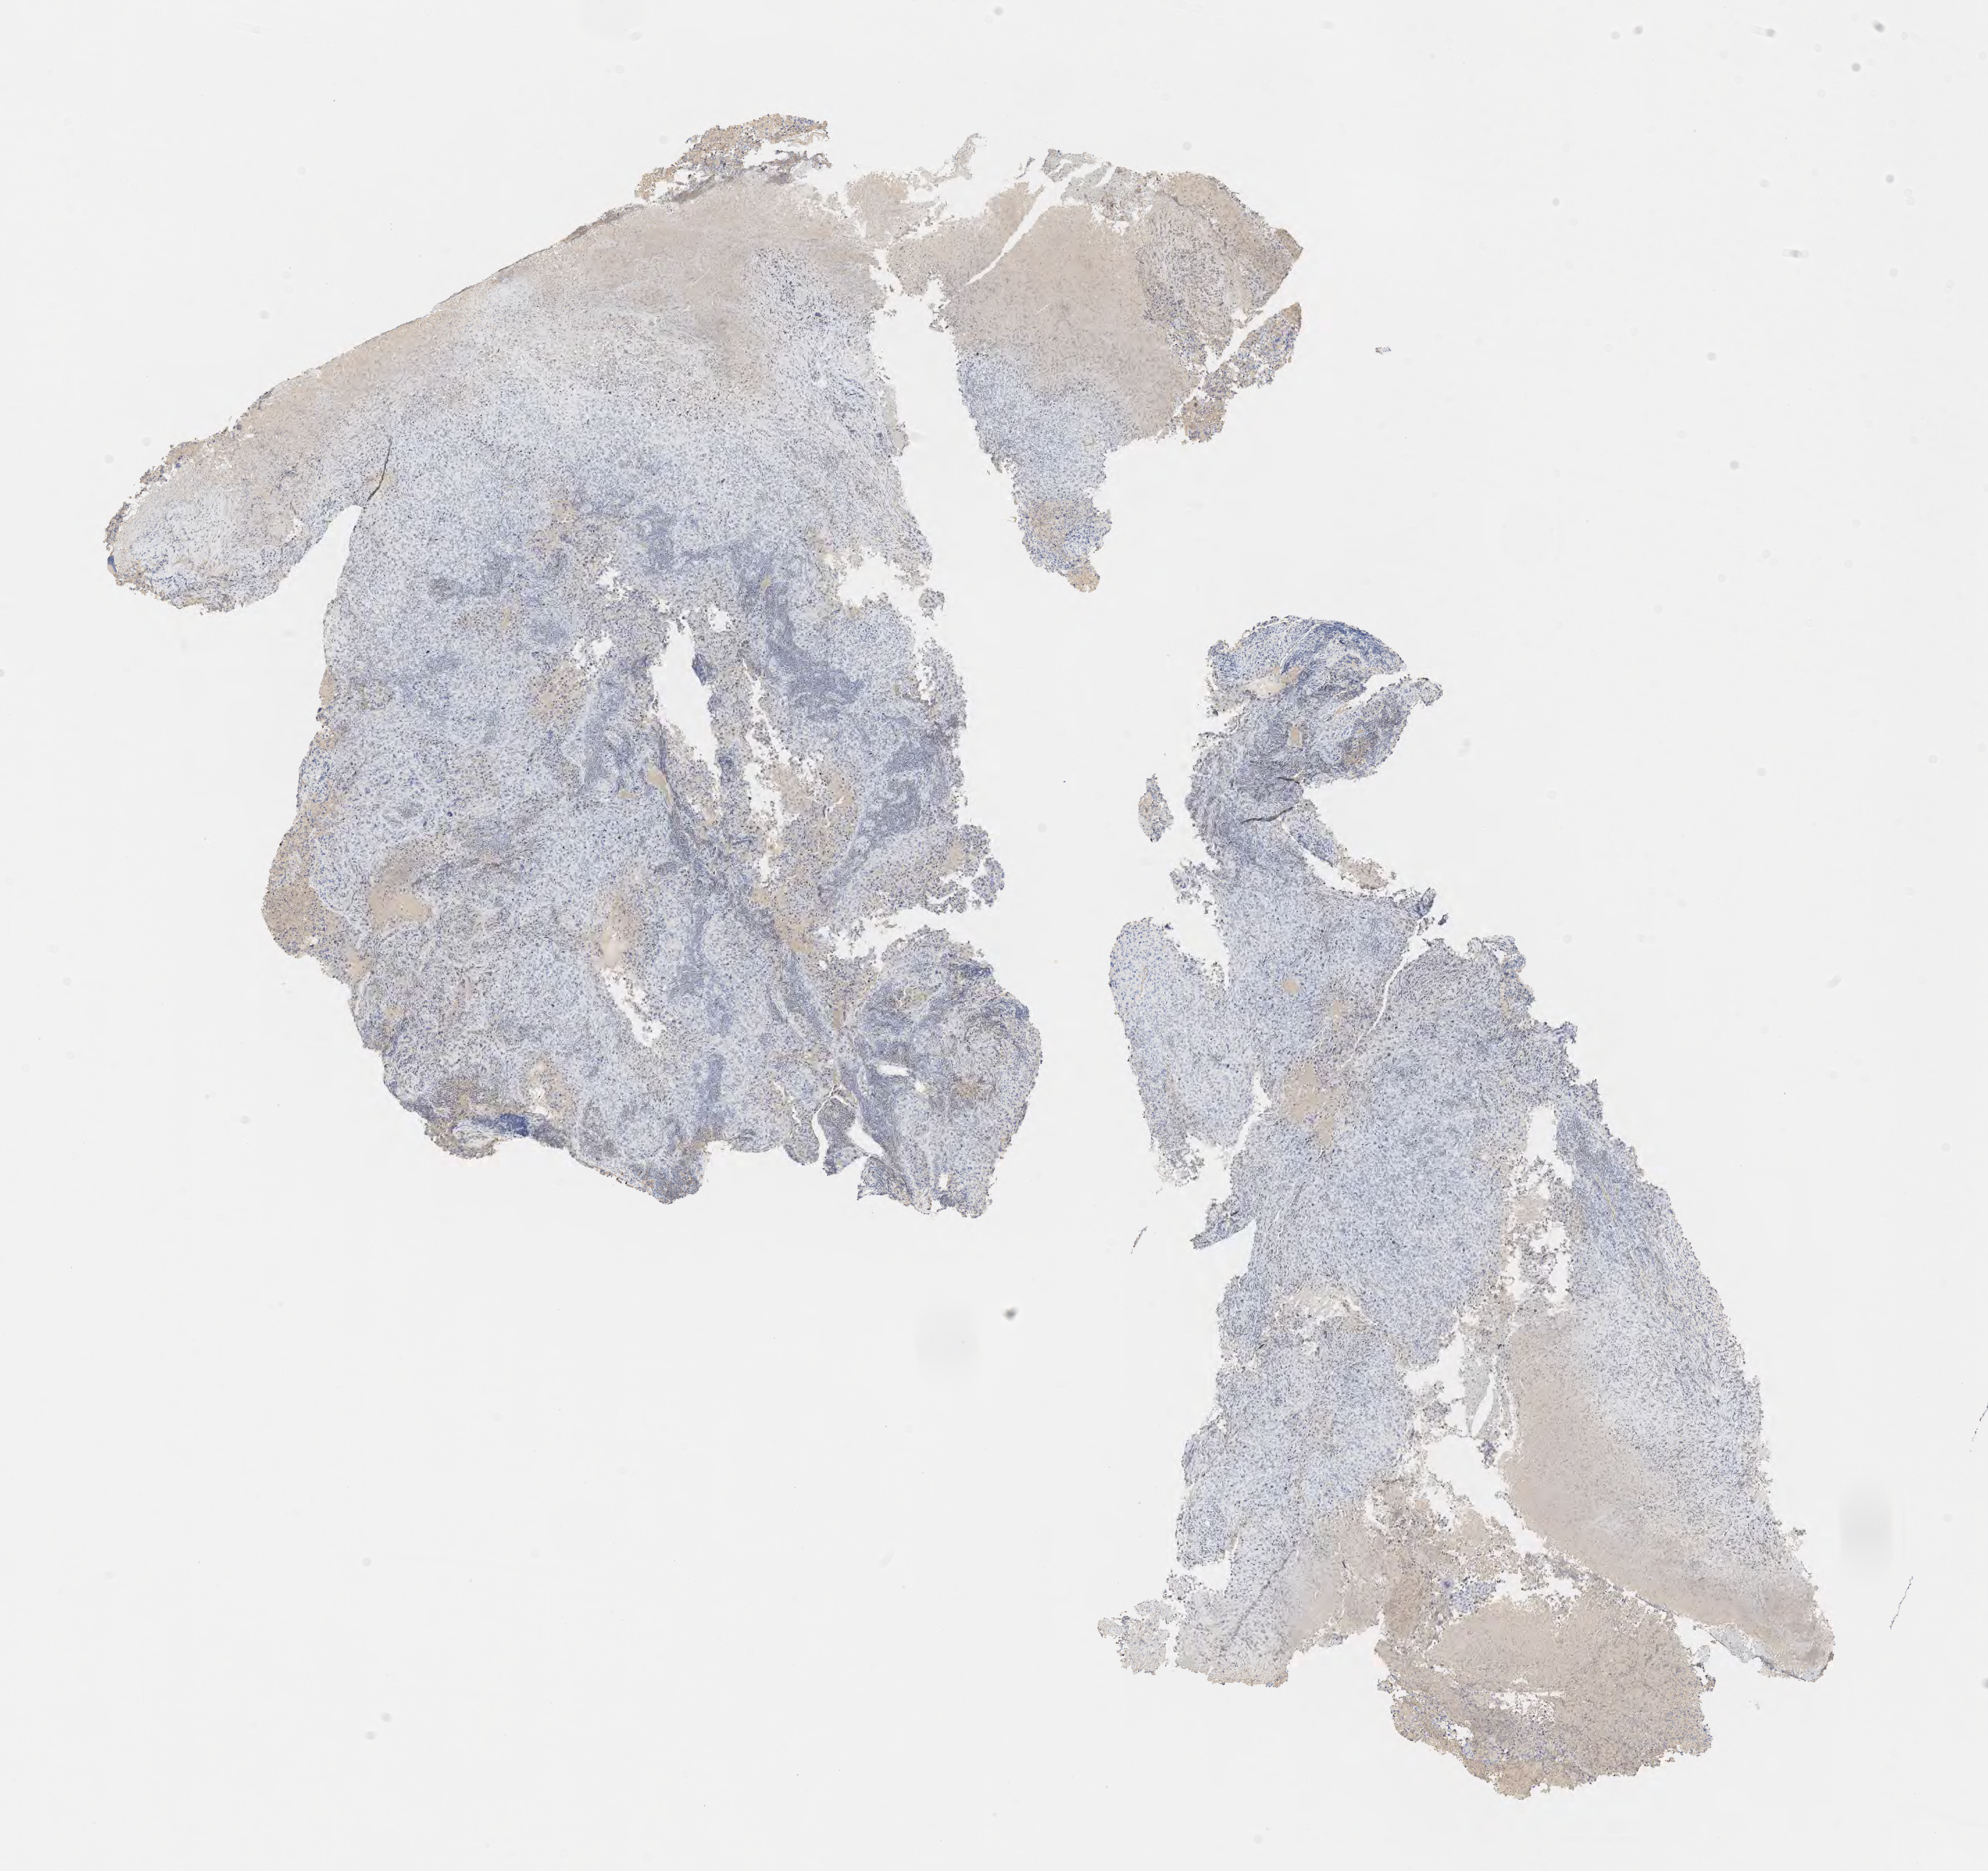
IHC for Ber-EP4, whole-slide image — a low-resolution overview of the entire scanned area, about 11.6 x 10.9 mm, specimen: tumor tissue, anatomic site: cervix. Female patient, aged 38.
Diagnosis: Squamous cell carcinoma, large cell, nonkeratinizing, NOS.